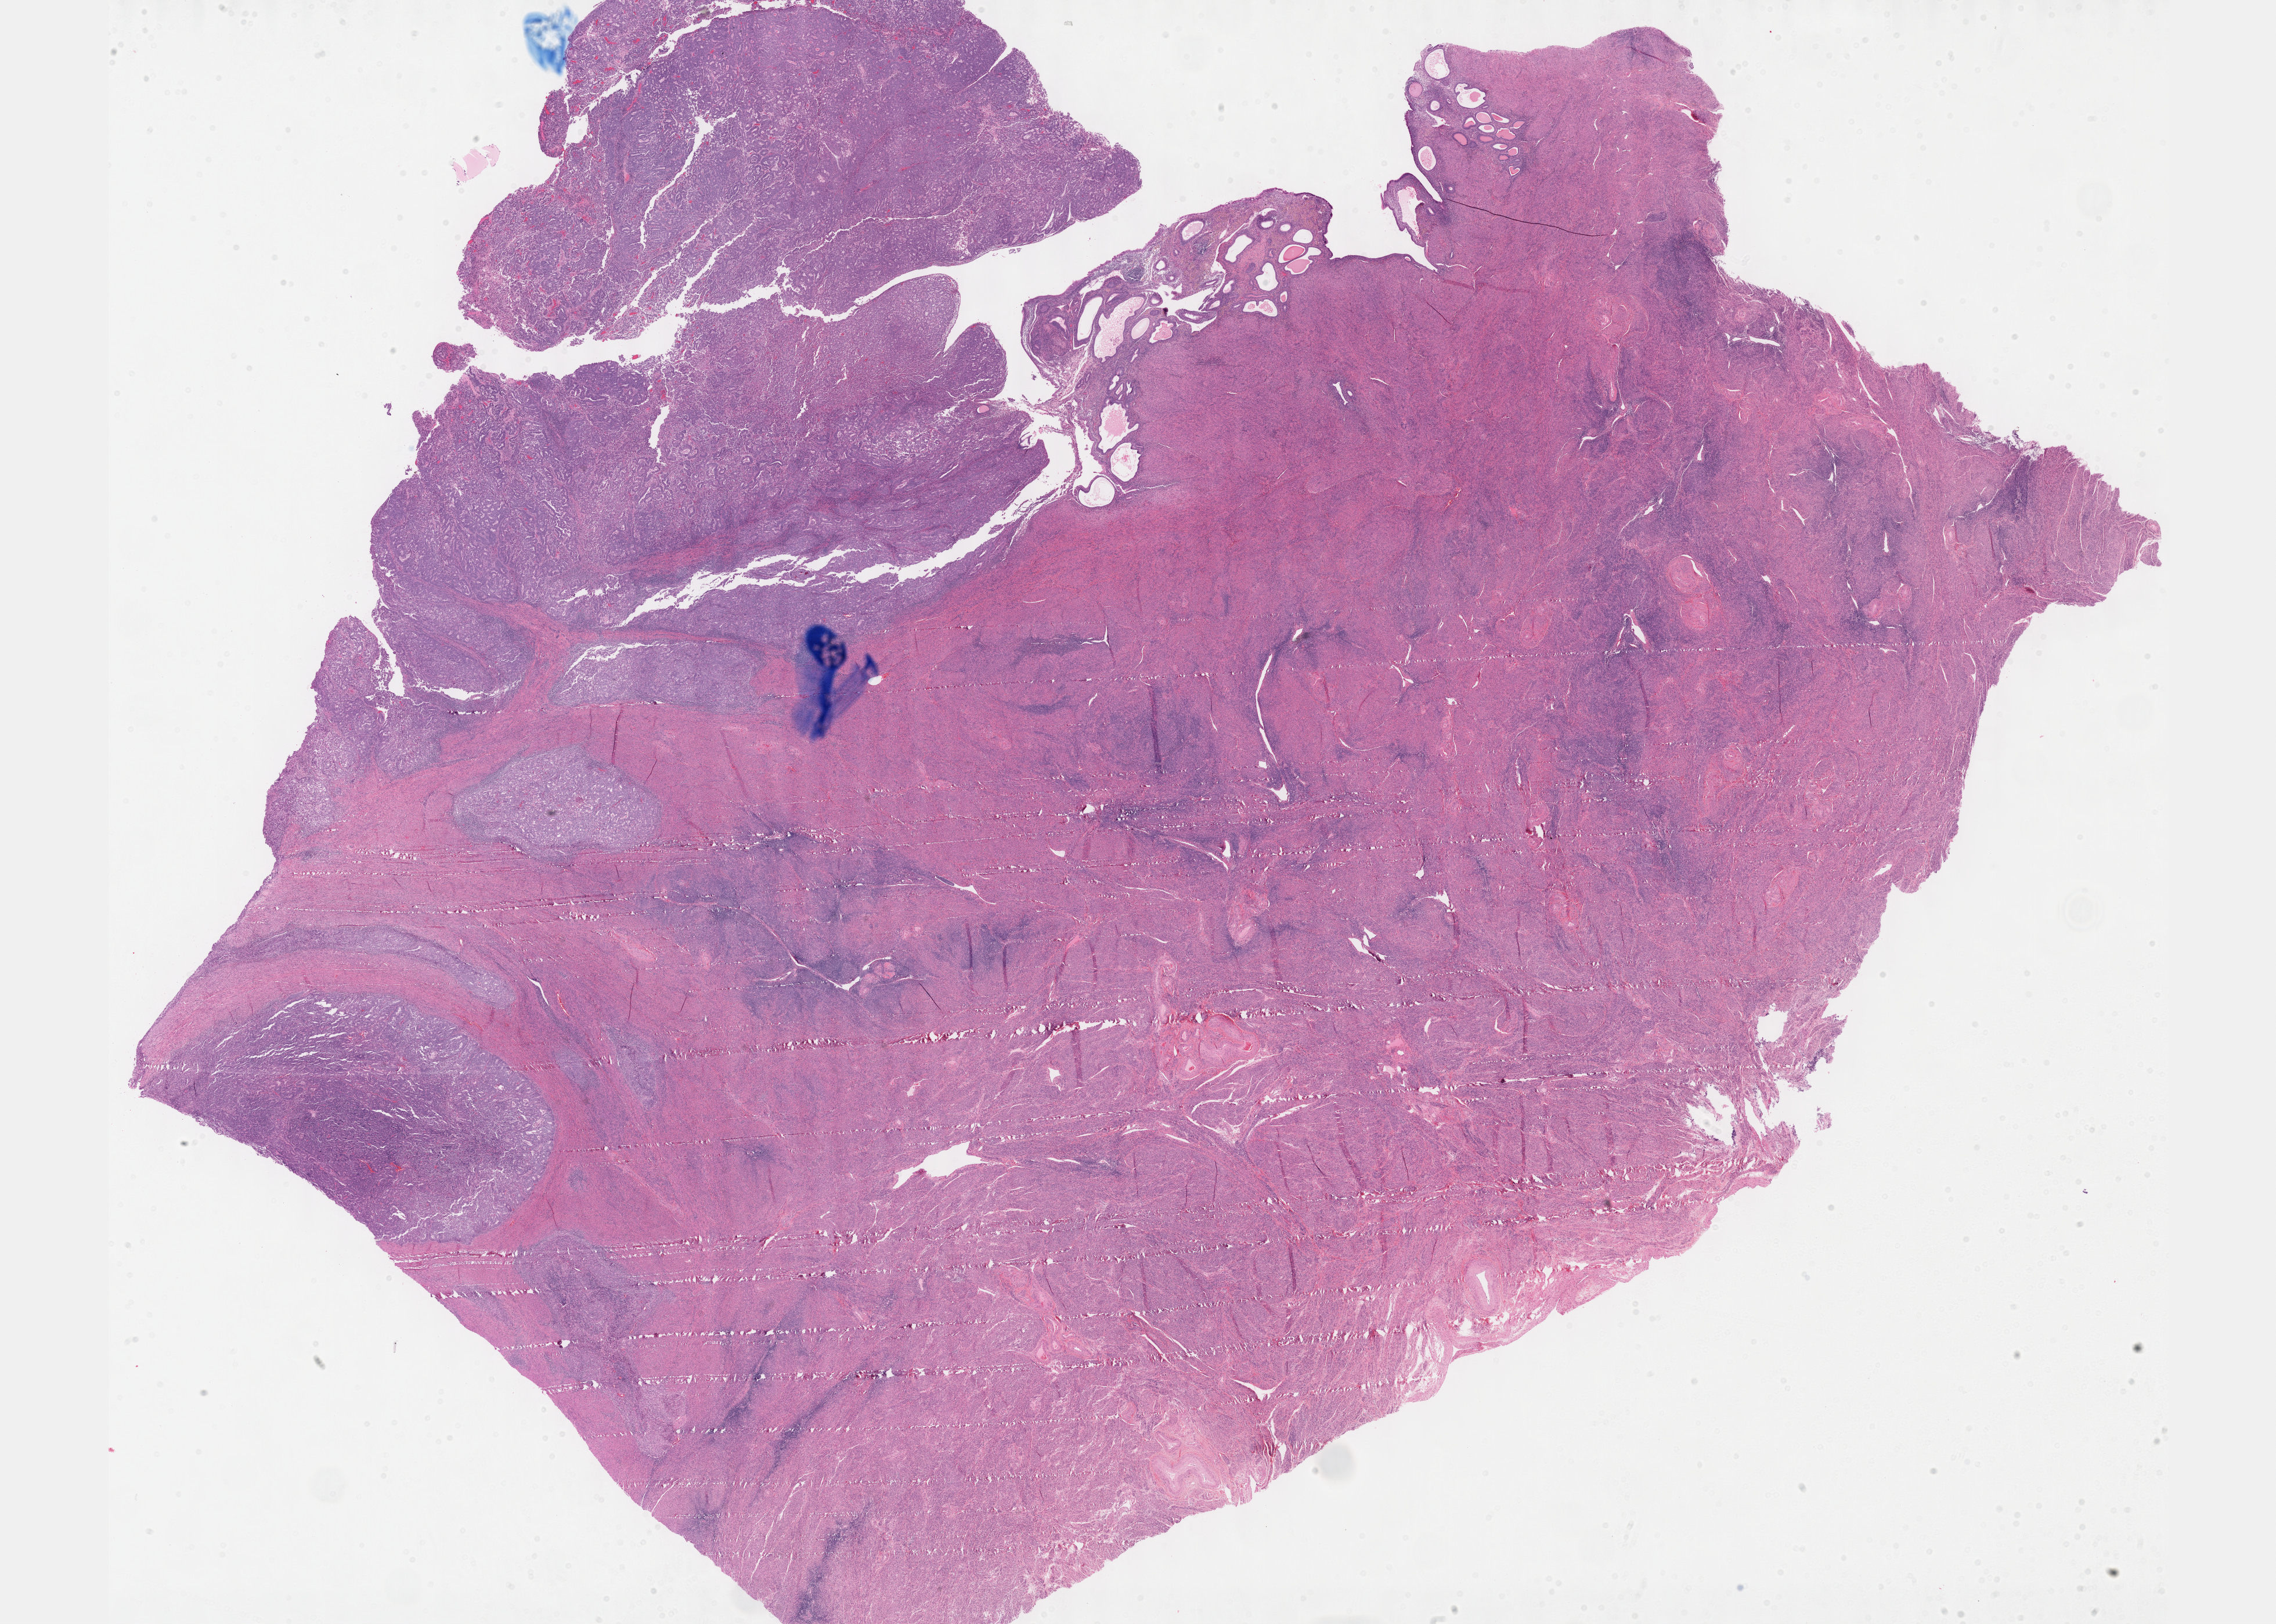
Whole-slide histology image, Hematoxylin and eosin (H&E) stained — shown as a low-resolution overview of the whole scanned area (about 31.7 x 22.6 mm, acquisition: 40x scan); FFPE section; sample: primary tumour, uterus. Female patient; age at initial diagnosis 74 years. Histologic grade: G2 (moderately differentiated).
Histologic diagnosis: Endometrioid adenocarcinoma, NOS (endometrium). FIGO stage: IA.